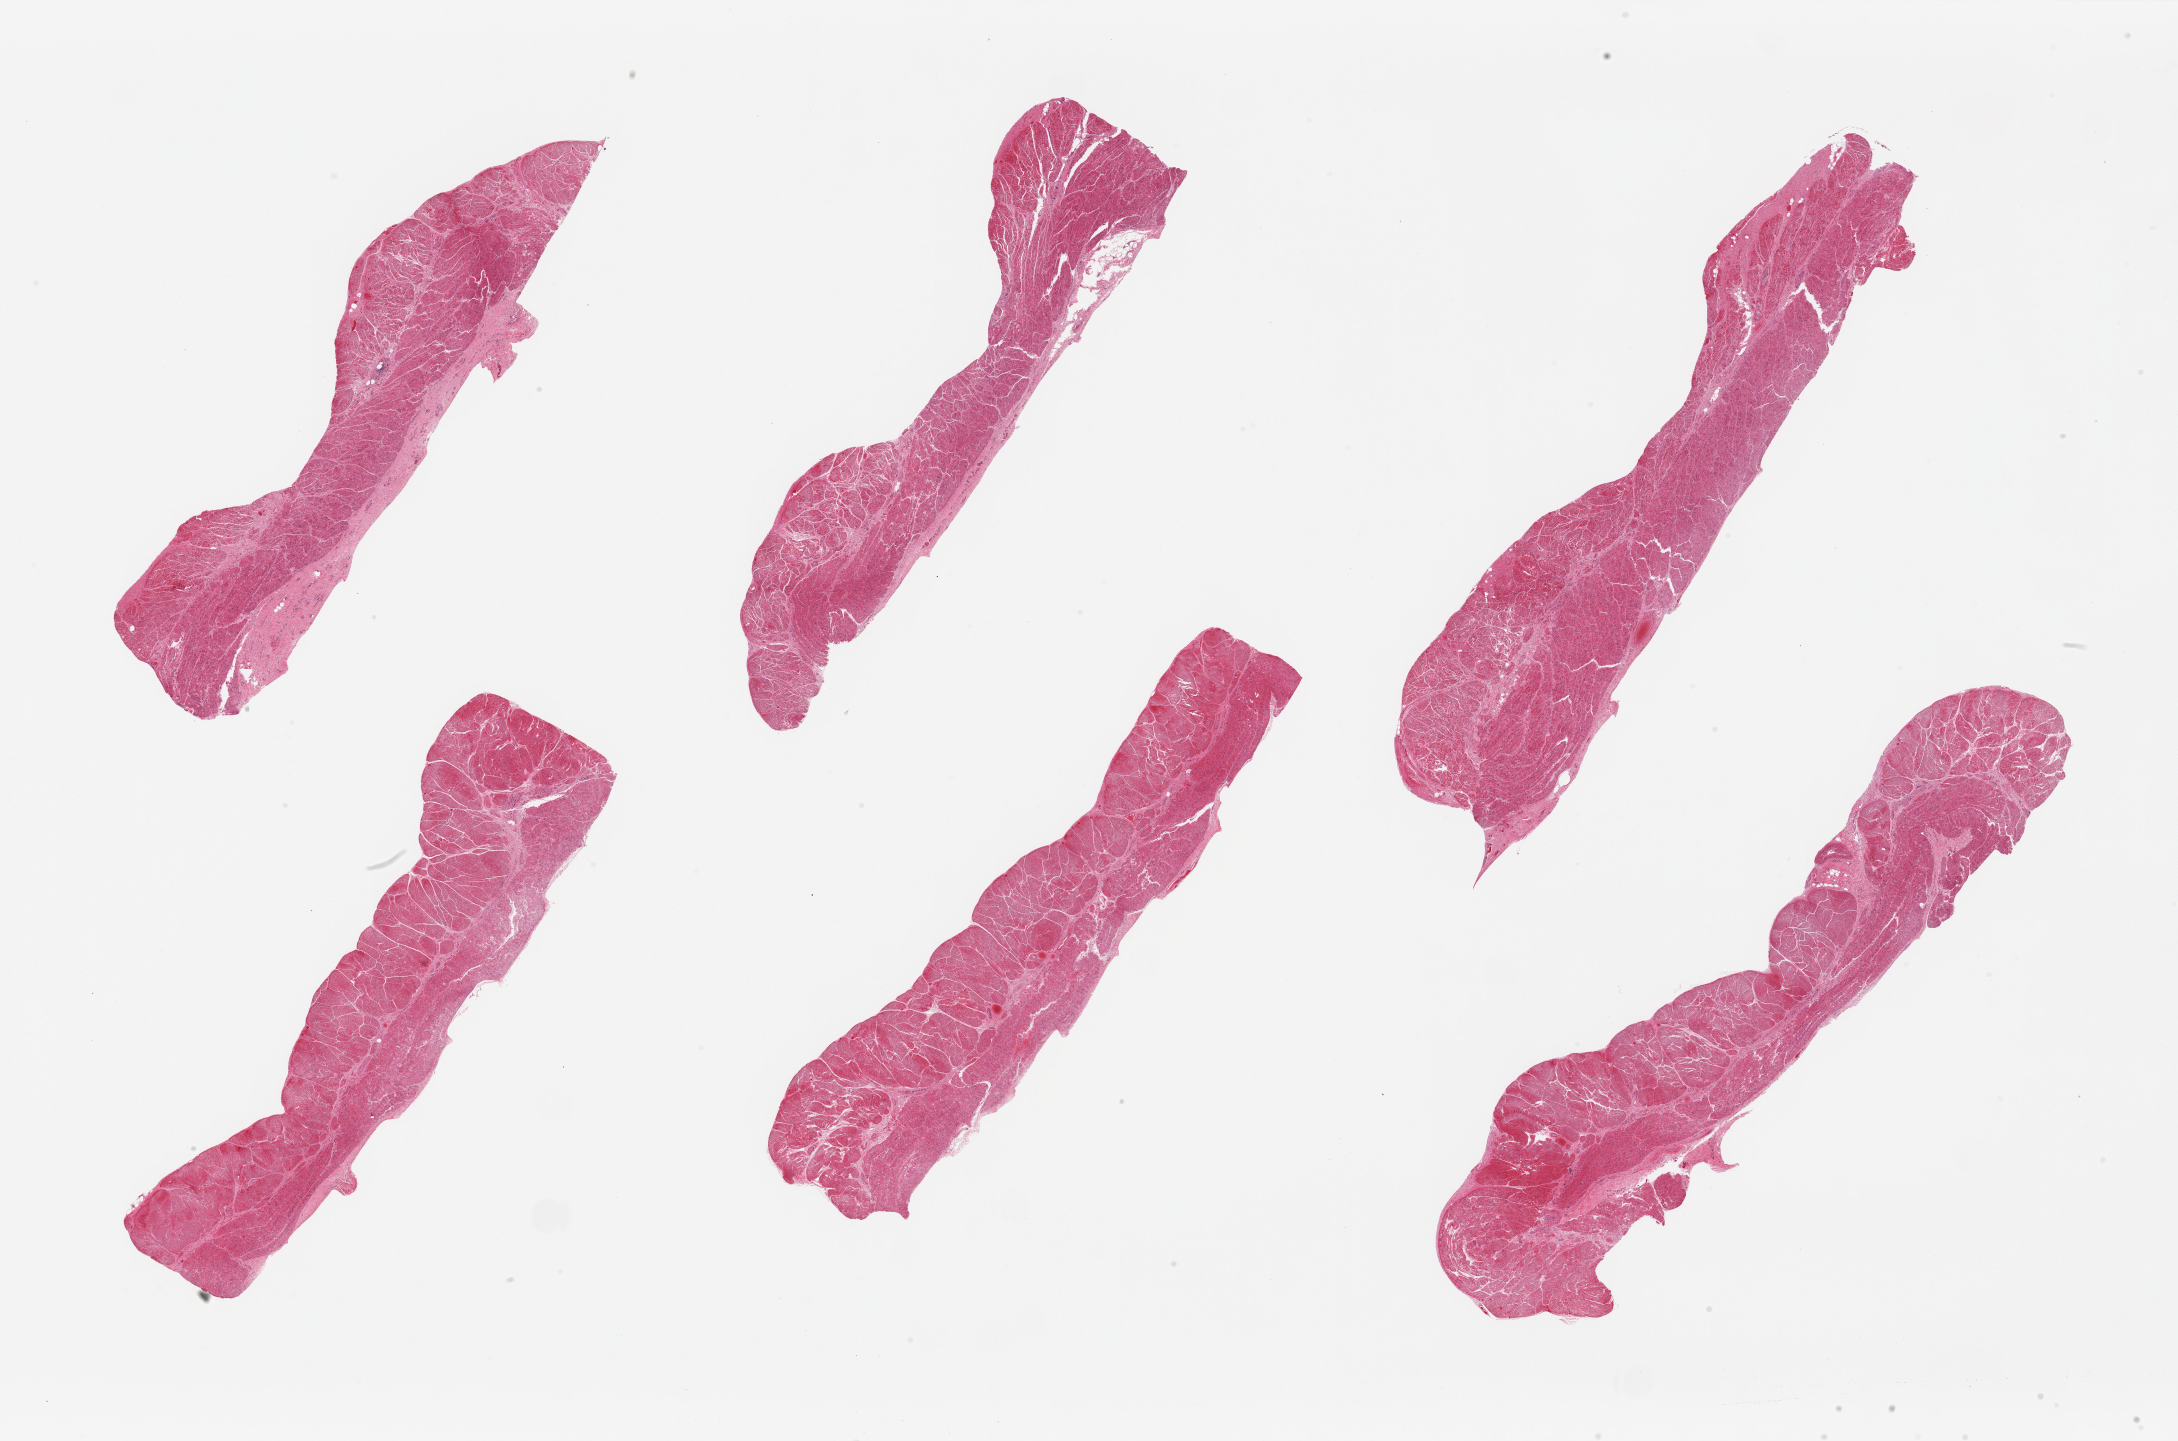
Digitized haematoxylin and eosin-stained section, brightfield, shown as a low-resolution overview of the whole scanned area (about 34.5 x 22.8 mm). PAXgene-fixed, paraffin-embedded tissue. Target tissue: esophageal muscle. Tissue donor sample. Donor sex: male.
Review note (as recorded): 6 pieces; well trimmed.